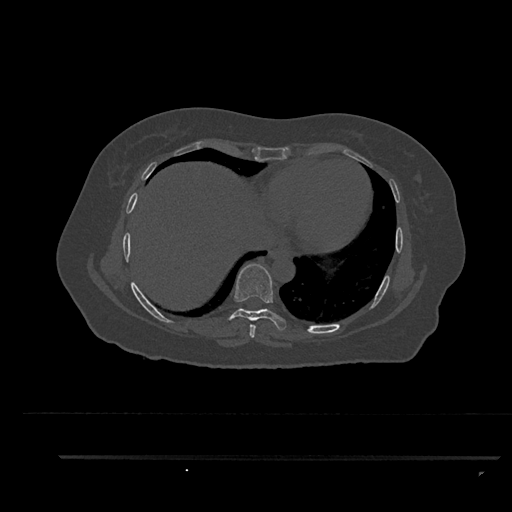
CT including the spine, one axial slice; position 462 of 797 along the scan axis; 120 kVp; bone window (W 1800 / L 400 HU); 512 × 512 image matrix. Patient: female, 44 years. Case-level facts recorded for this patient, not image findings: primary cancer: renal; vertebrae with lytic lesions (as recorded): L1.
Annotated regions visible in this slice (semi-automatically segmented with operator editing):
- T7 vertebra: bounding box (x1, y1, x2, y2) in pixels: (249, 324, 256, 338)
- T8 vertebra: (227, 264, 286, 331)